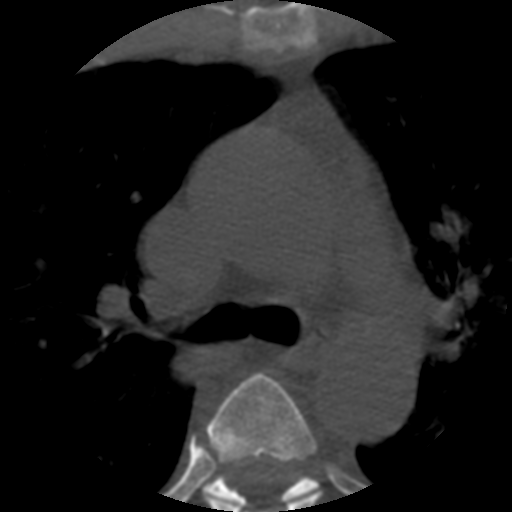
CT including the spine, one axial slice; slice 387 of 508 in the series (ordered by position); reconstruction kernel STANDARD; bone window (W 1800 / L 400 HU); 1.25 mm slice thickness; 512 × 512 image matrix, field of view 160 × 160 mm. Patient age 57 years. From the clinical record (not read from this slice): primary cancer: prostate.
Structures marked on this image (semi-automatic segmentation, software-assisted and operator-edited):
- T4 vertebra: box from (x=202, y=372) to (x=320, y=512) px
- T5 vertebra: (x=206, y=474)–(x=319, y=507)